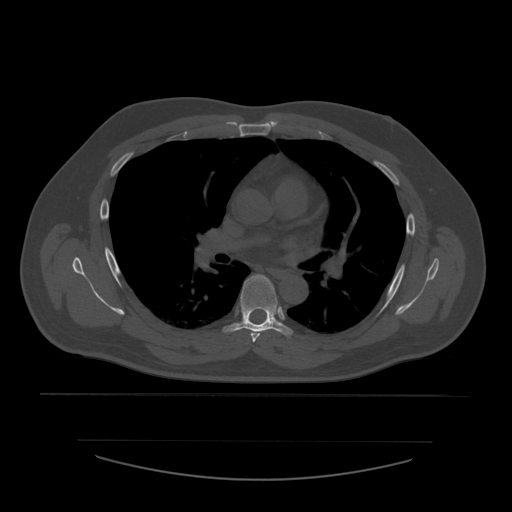
CT including the spine, one axial slice. Position 382 of 532 along the scan axis. Reconstruction kernel STANDARD. Bone window (W 1800 / L 400 HU). 1.25 mm slice thickness. 512 × 512 image matrix, field of view 441 × 441 mm. Patient age 44 years. Case-level facts recorded for this patient, not image findings: primary cancer: soft tissue sarcoma.
Outlined on this slice (semi-automatic segmentation, software-assisted and operator-edited):
- T5 vertebra: bounding box [x1, y1, x2, y2] px = [250, 332, 261, 342]
- T6 vertebra: [223, 275, 293, 336]